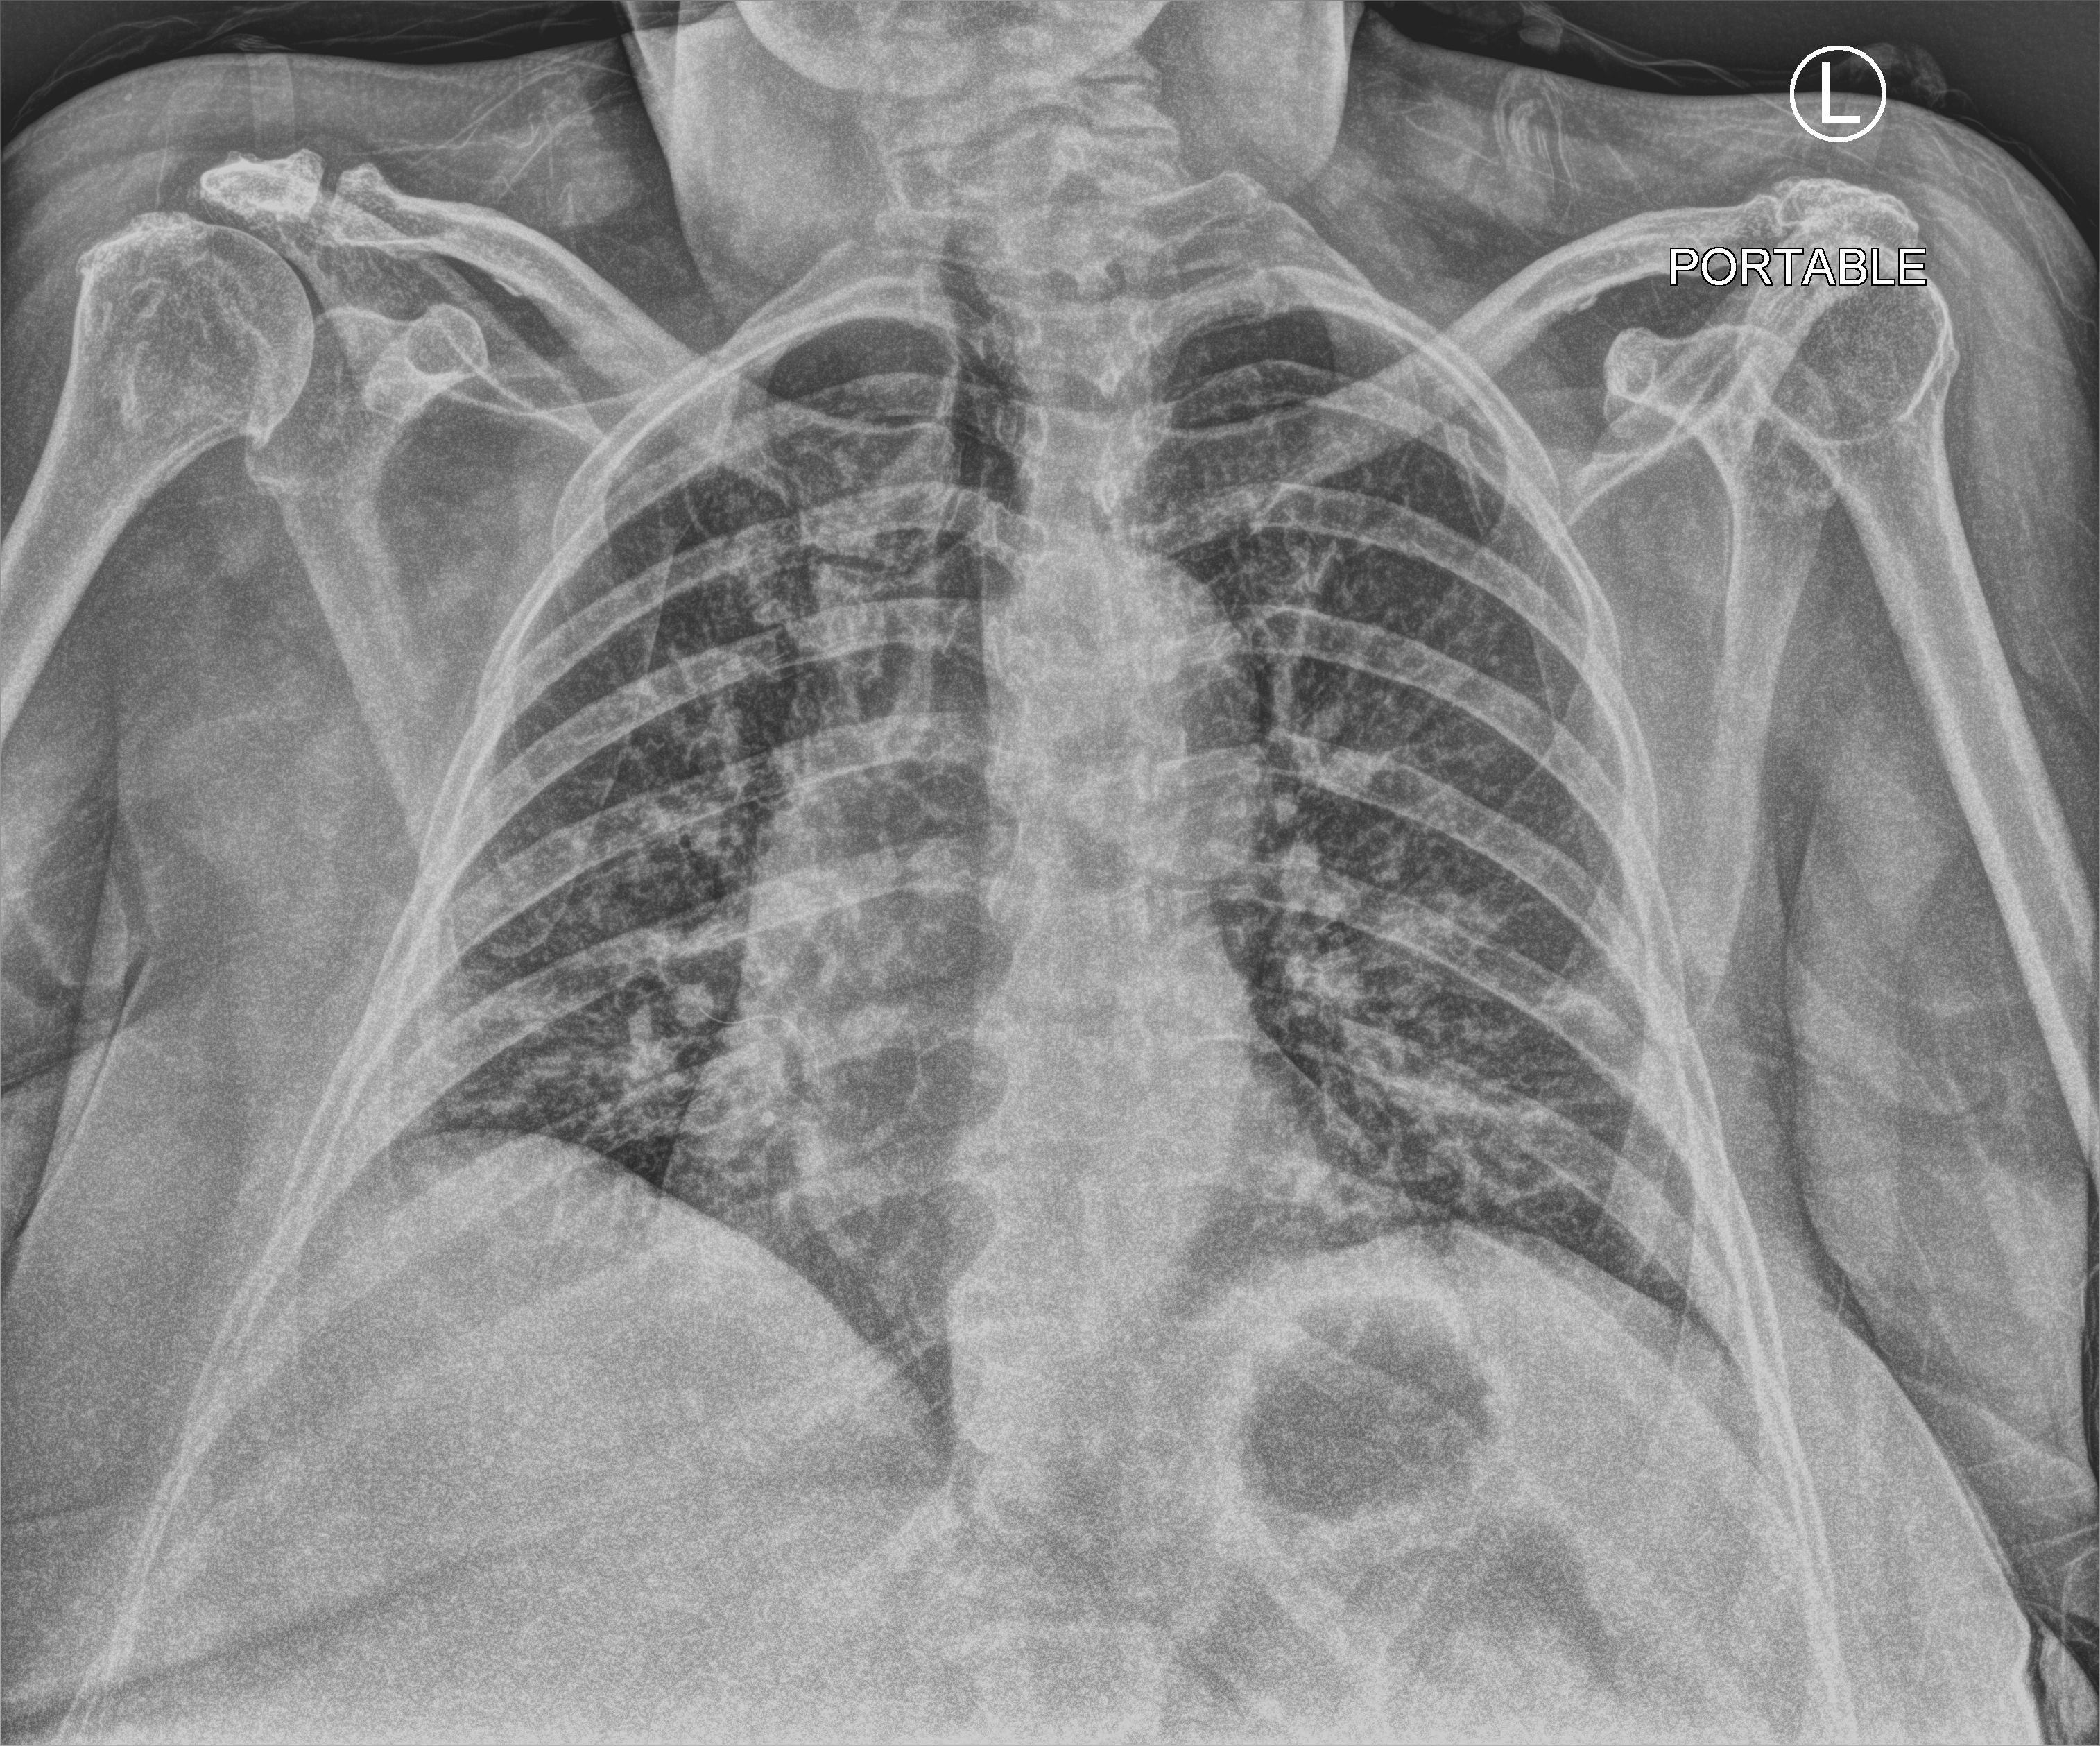
Chest X-ray (portable); anteroposterior (AP) projection. Patient hospitalised with COVID-19; female, aged 60–74 years.
From the hospital-stay record, not from the radiograph (when in the stay this image was taken is not recorded):
- admitted to intensive care during this hospital stay: no
- mechanically ventilated during this hospital stay: no
- length of hospital stay: 10 days